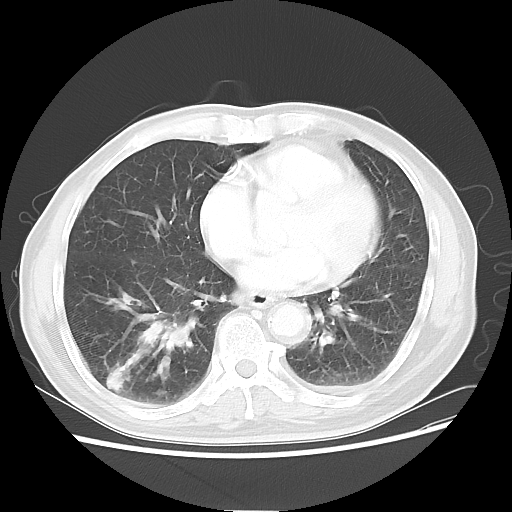
Chest CT, one axial slice; slice 24 of 58 in the series (ordered by position); reconstruction kernel LUNG; lung window (W 1500 / L -600 HU); 512 × 512 image matrix. Patient: male, 74 years. From the clinical record (not read from this slice): clinical TNM (as recorded): T1c N1 M1.
Annotated regions visible in this slice (rectangle marked by the reading radiologist):
- lung tumour (recorded histology: adenocarcinoma): bounding box [x1, y1, x2, y2] px = [128, 291, 200, 371]